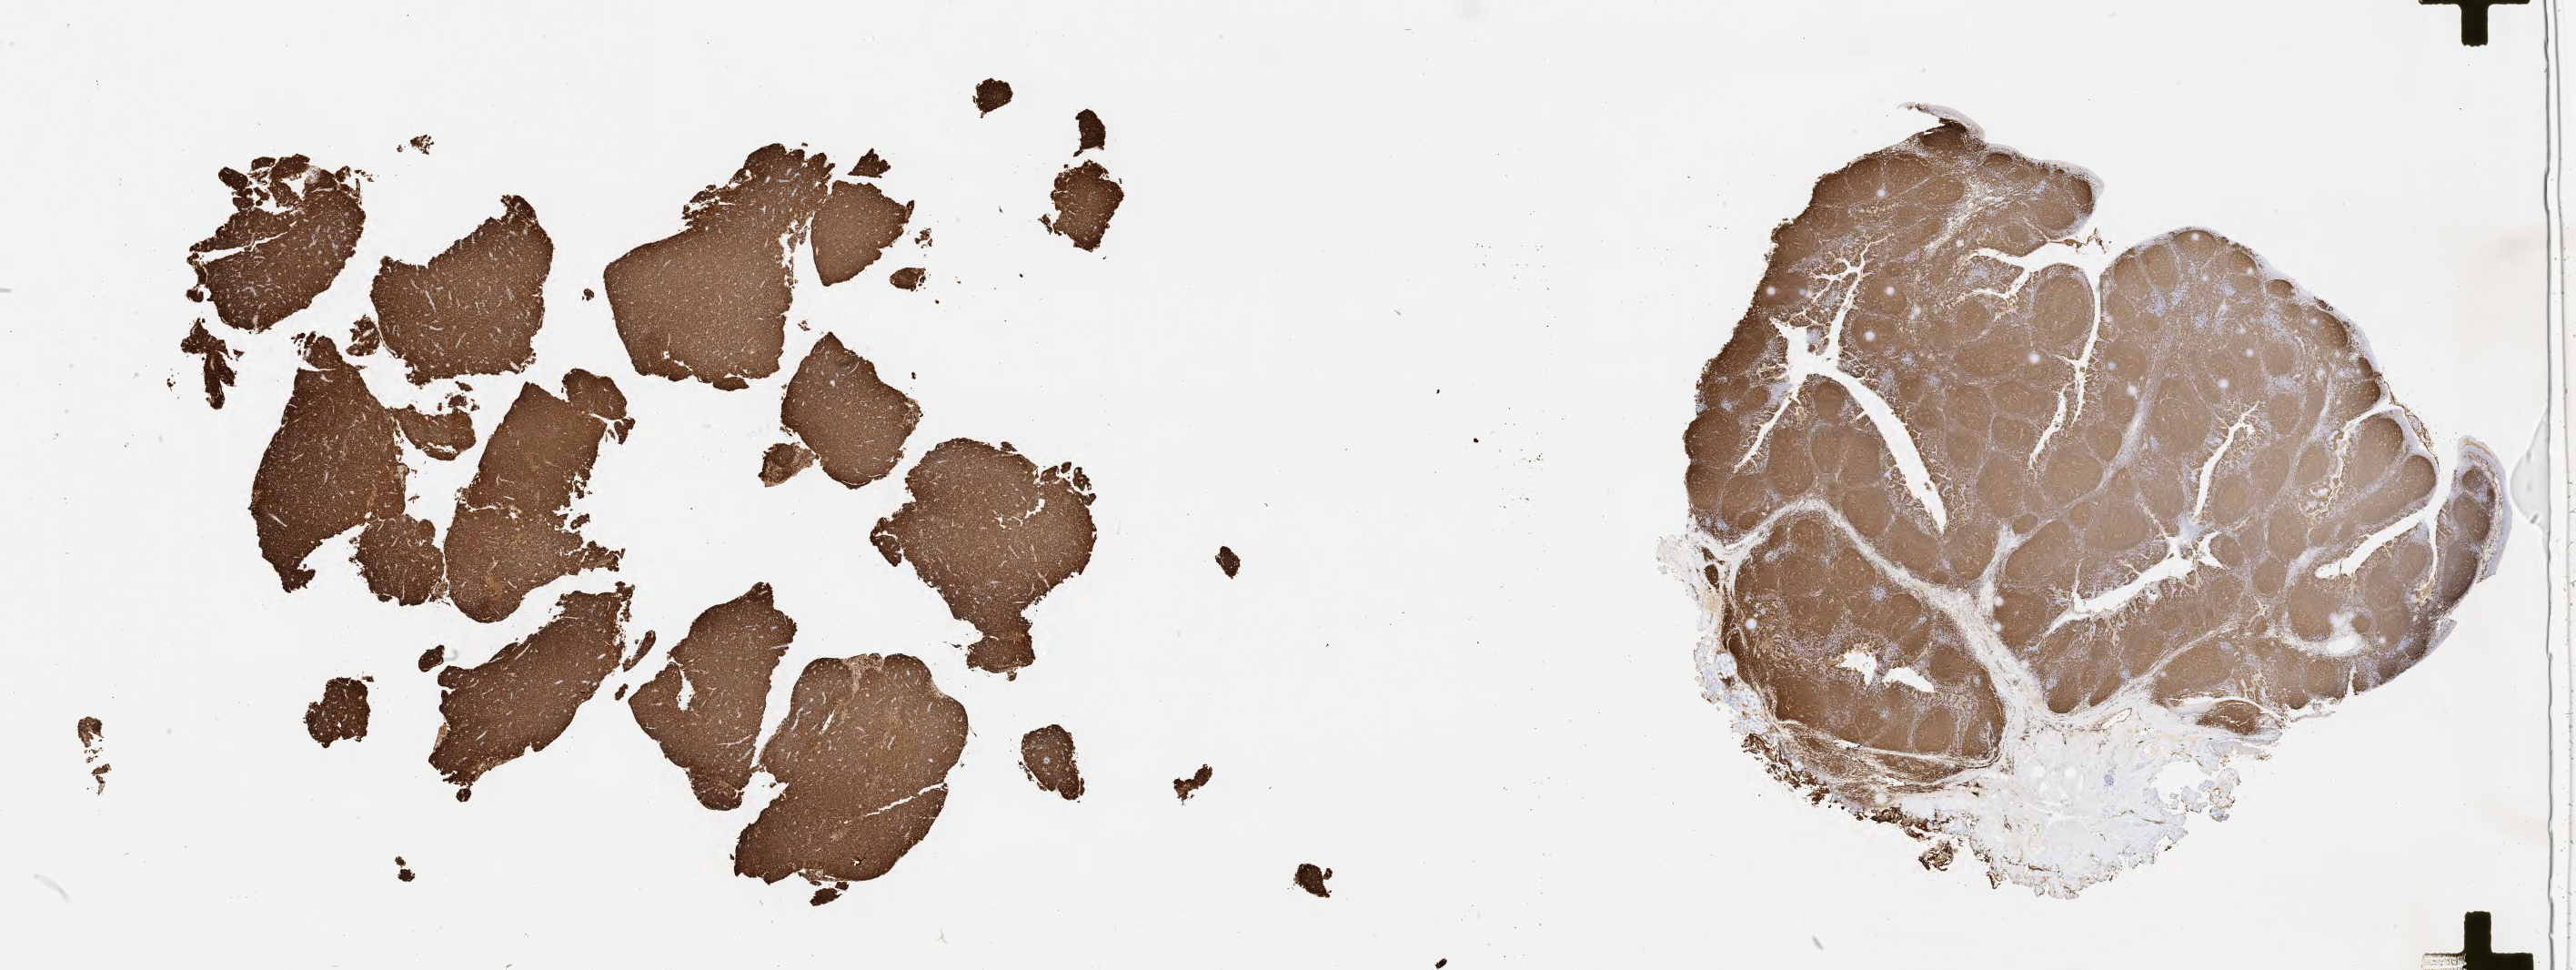
IHC for CD20, whole-slide image, shown as a low-resolution overview of the whole scanned area (about 45.8 x 17.2 mm), specimen: tumor tissue, anatomic site: lymph node. Patient female; age 50 years.
- diagnosis: Diffuse large B-cell lymphoma, NOS